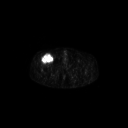
FDG PET of an extremity soft-tissue mass (from a PET/CT study), one axial slice. Position 301 of 311 along the scan axis. 3.27 mm slice thickness. 128 × 128 image matrix. Patient: male, 56 years. Case-level facts recorded for this patient, not image findings: histological type: pleiomorphic leiomyosarcoma; grade: intermediate; site of the primary tumour: right thigh.
Structures marked on this image (expert contour drawn on MRI and transferred to this co-registered scan by the dataset authors):
- gross tumour volume including surrounding oedema: bounding box (x1, y1, x2, y2) in pixels: (41, 53, 53, 64)
- gross tumour volume (mass): (41, 54, 53, 64)